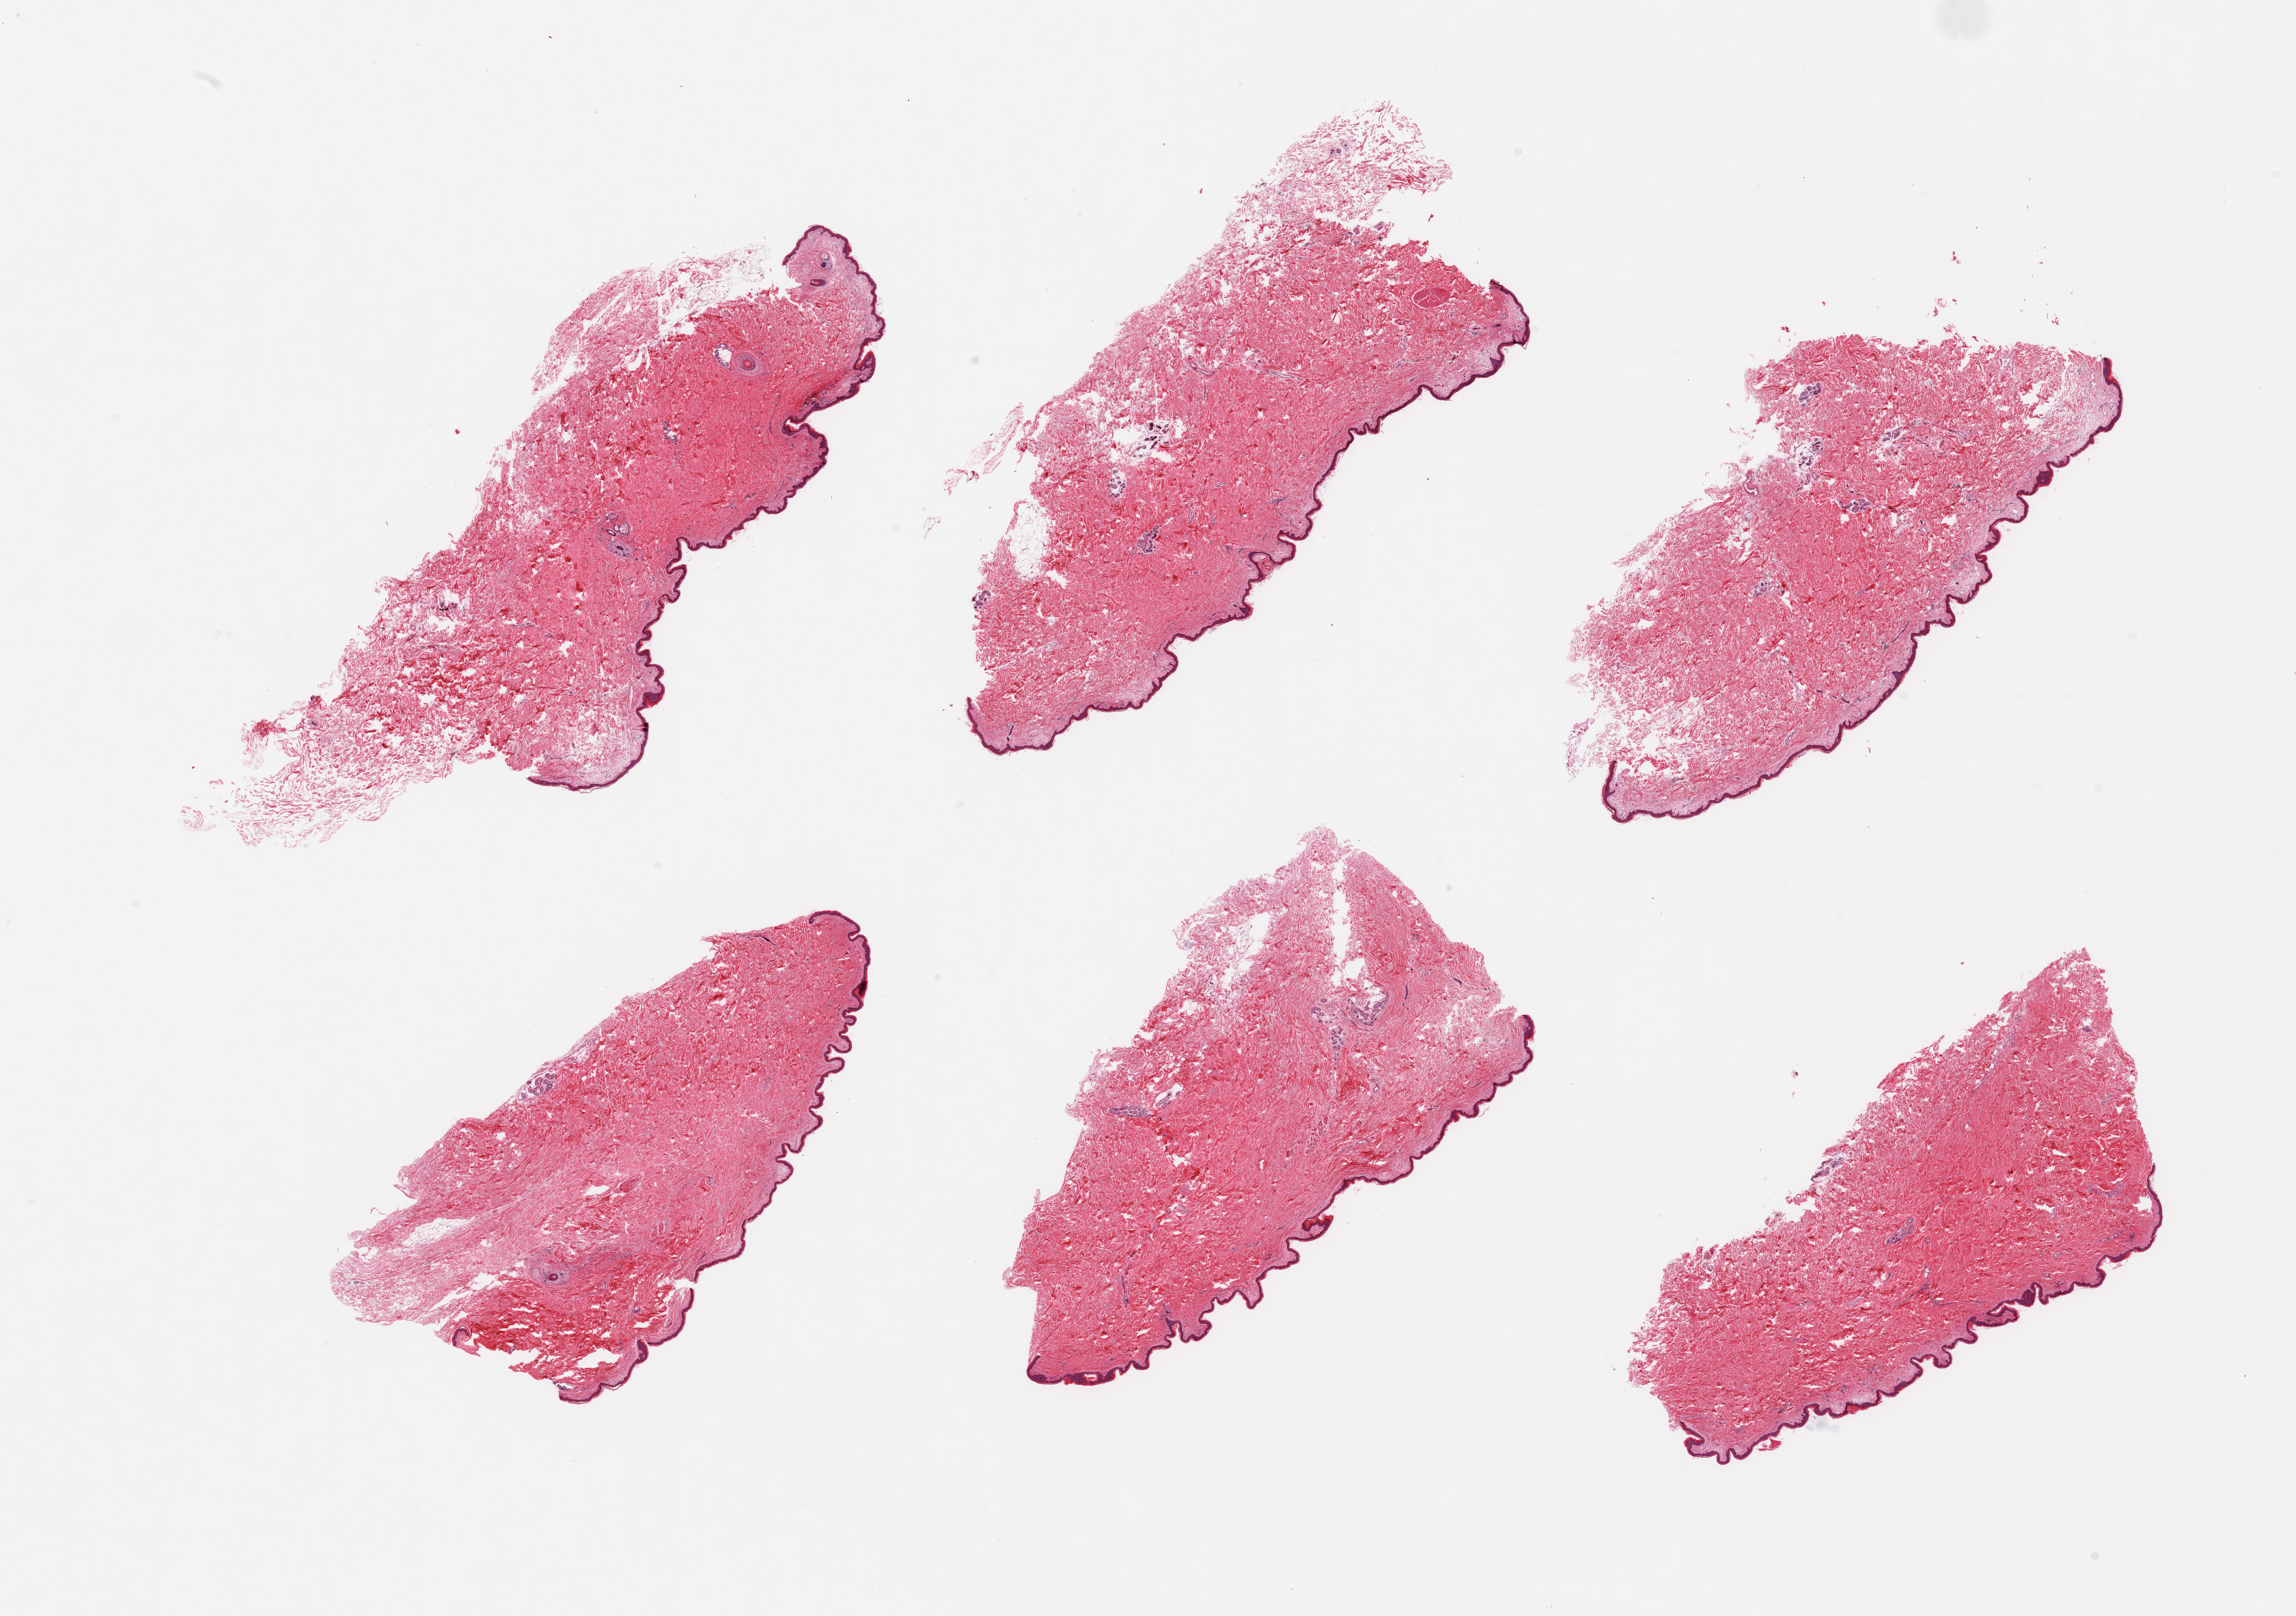
Digitized H&E-stained section — whole scanned area (about 26.6 x 18.7 mm) shown as a low-resolution overview. PAXgene-fixed paraffin-embedded (PFPE) section. Sampled site (target tissue): skin of suprapubic region. Tissue donor sample. Donor: male.
Review note (as recorded): 6 pieces, minimal dermal fat; squamous epithelium is ~30-40 microns.